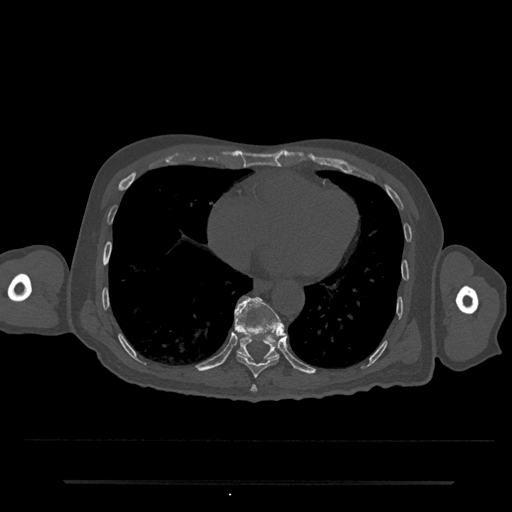
CT including the spine, one axial slice; position 345 of 797 along the scan axis; 120 kVp; bone window (W 1800 / L 400 HU); 0.5 mm slice thickness; 512 × 512 image matrix, field of view 427 × 427 mm. Patient: male, 74 years. From the clinical record (not read from this slice): primary cancer: prostate.
Structures marked on this image (semi-automatically segmented with operator editing):
- T10 vertebra: bounding box <234,296,285,361> (left, top, right, bottom; pixels)
- T8 vertebra: <250,385,258,392>
- T9 vertebra: <235,310,279,378>